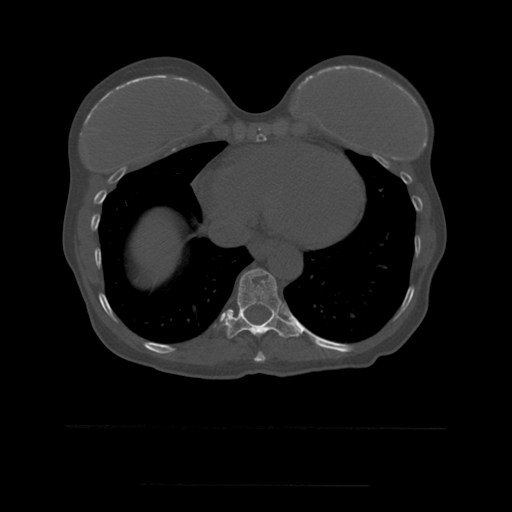
CT including the spine, one axial slice; slice 304 of 544 in the series (ordered by position); bone window (W 1800 / L 400 HU); 512 × 512 image matrix. Patient age 58 years. Case-level facts recorded for this patient, not image findings: primary cancer: lung.
Annotated regions visible in this slice (semi-automatic segmentation, software-assisted and operator-edited):
- T10 vertebra: bounding box <224,269,298,338> (left, top, right, bottom; pixels)
- T9 vertebra: <254,352,266,362>